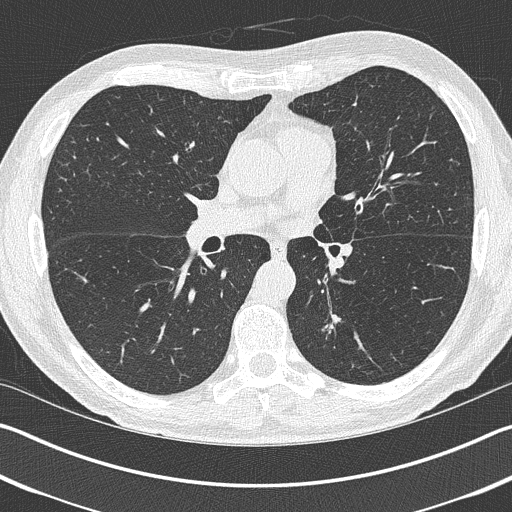
Low-dose screening chest CT, one axial slice; slice 225 of 402 in the series (ordered by position); lung window (W 1500 / L -600 HU); 512 × 512 image matrix, field of view 340 × 340 mm.
Outlined on this slice (outlined manually by an expert reader):
- lesion 1 (tumor, lower lobe of left lung): bounding box (x1, y1, x2, y2) in pixels: (323, 313, 341, 334)